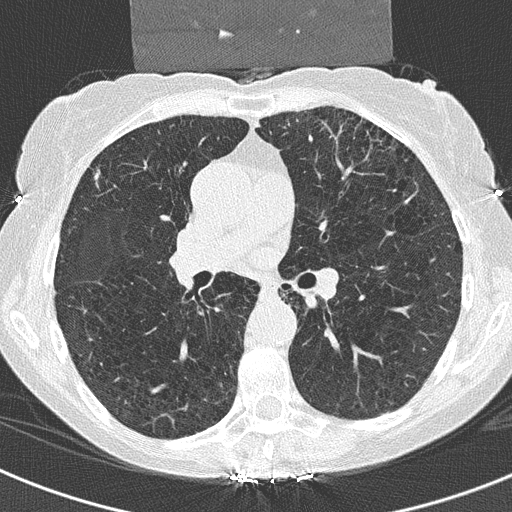
Low-dose screening chest CT, axial slice. Third screening round (two years after baseline). Lung window (W 1500 / L -600 HU). Slice 132 of 325 in the series. 512 × 512 image matrix. Female, age 70 years at enrolment. Current smoker at enrolment.
- Expert-annotated lung lesion, bounding box [x1, y1, x2, y2] px = [74, 159, 111, 194].
- The exam's reader record, not a measurement of the box and not confirmed to be the same lesion: non-calcified nodule or mass ≥4 mm, right middle lobe, 5 × 5 mm, spiculated (stellate) margins, ground glass attenuation, pre-existing on the prior screen: no.
- Official screen result: positive, other.
- Later outcome: lung cancer diagnosed 321 days after this screen — adenosquamous carcinoma, right upper lobe, poorly differentiated (G3), stage IA (AJCC 6th edition), 12 mm at pathology.